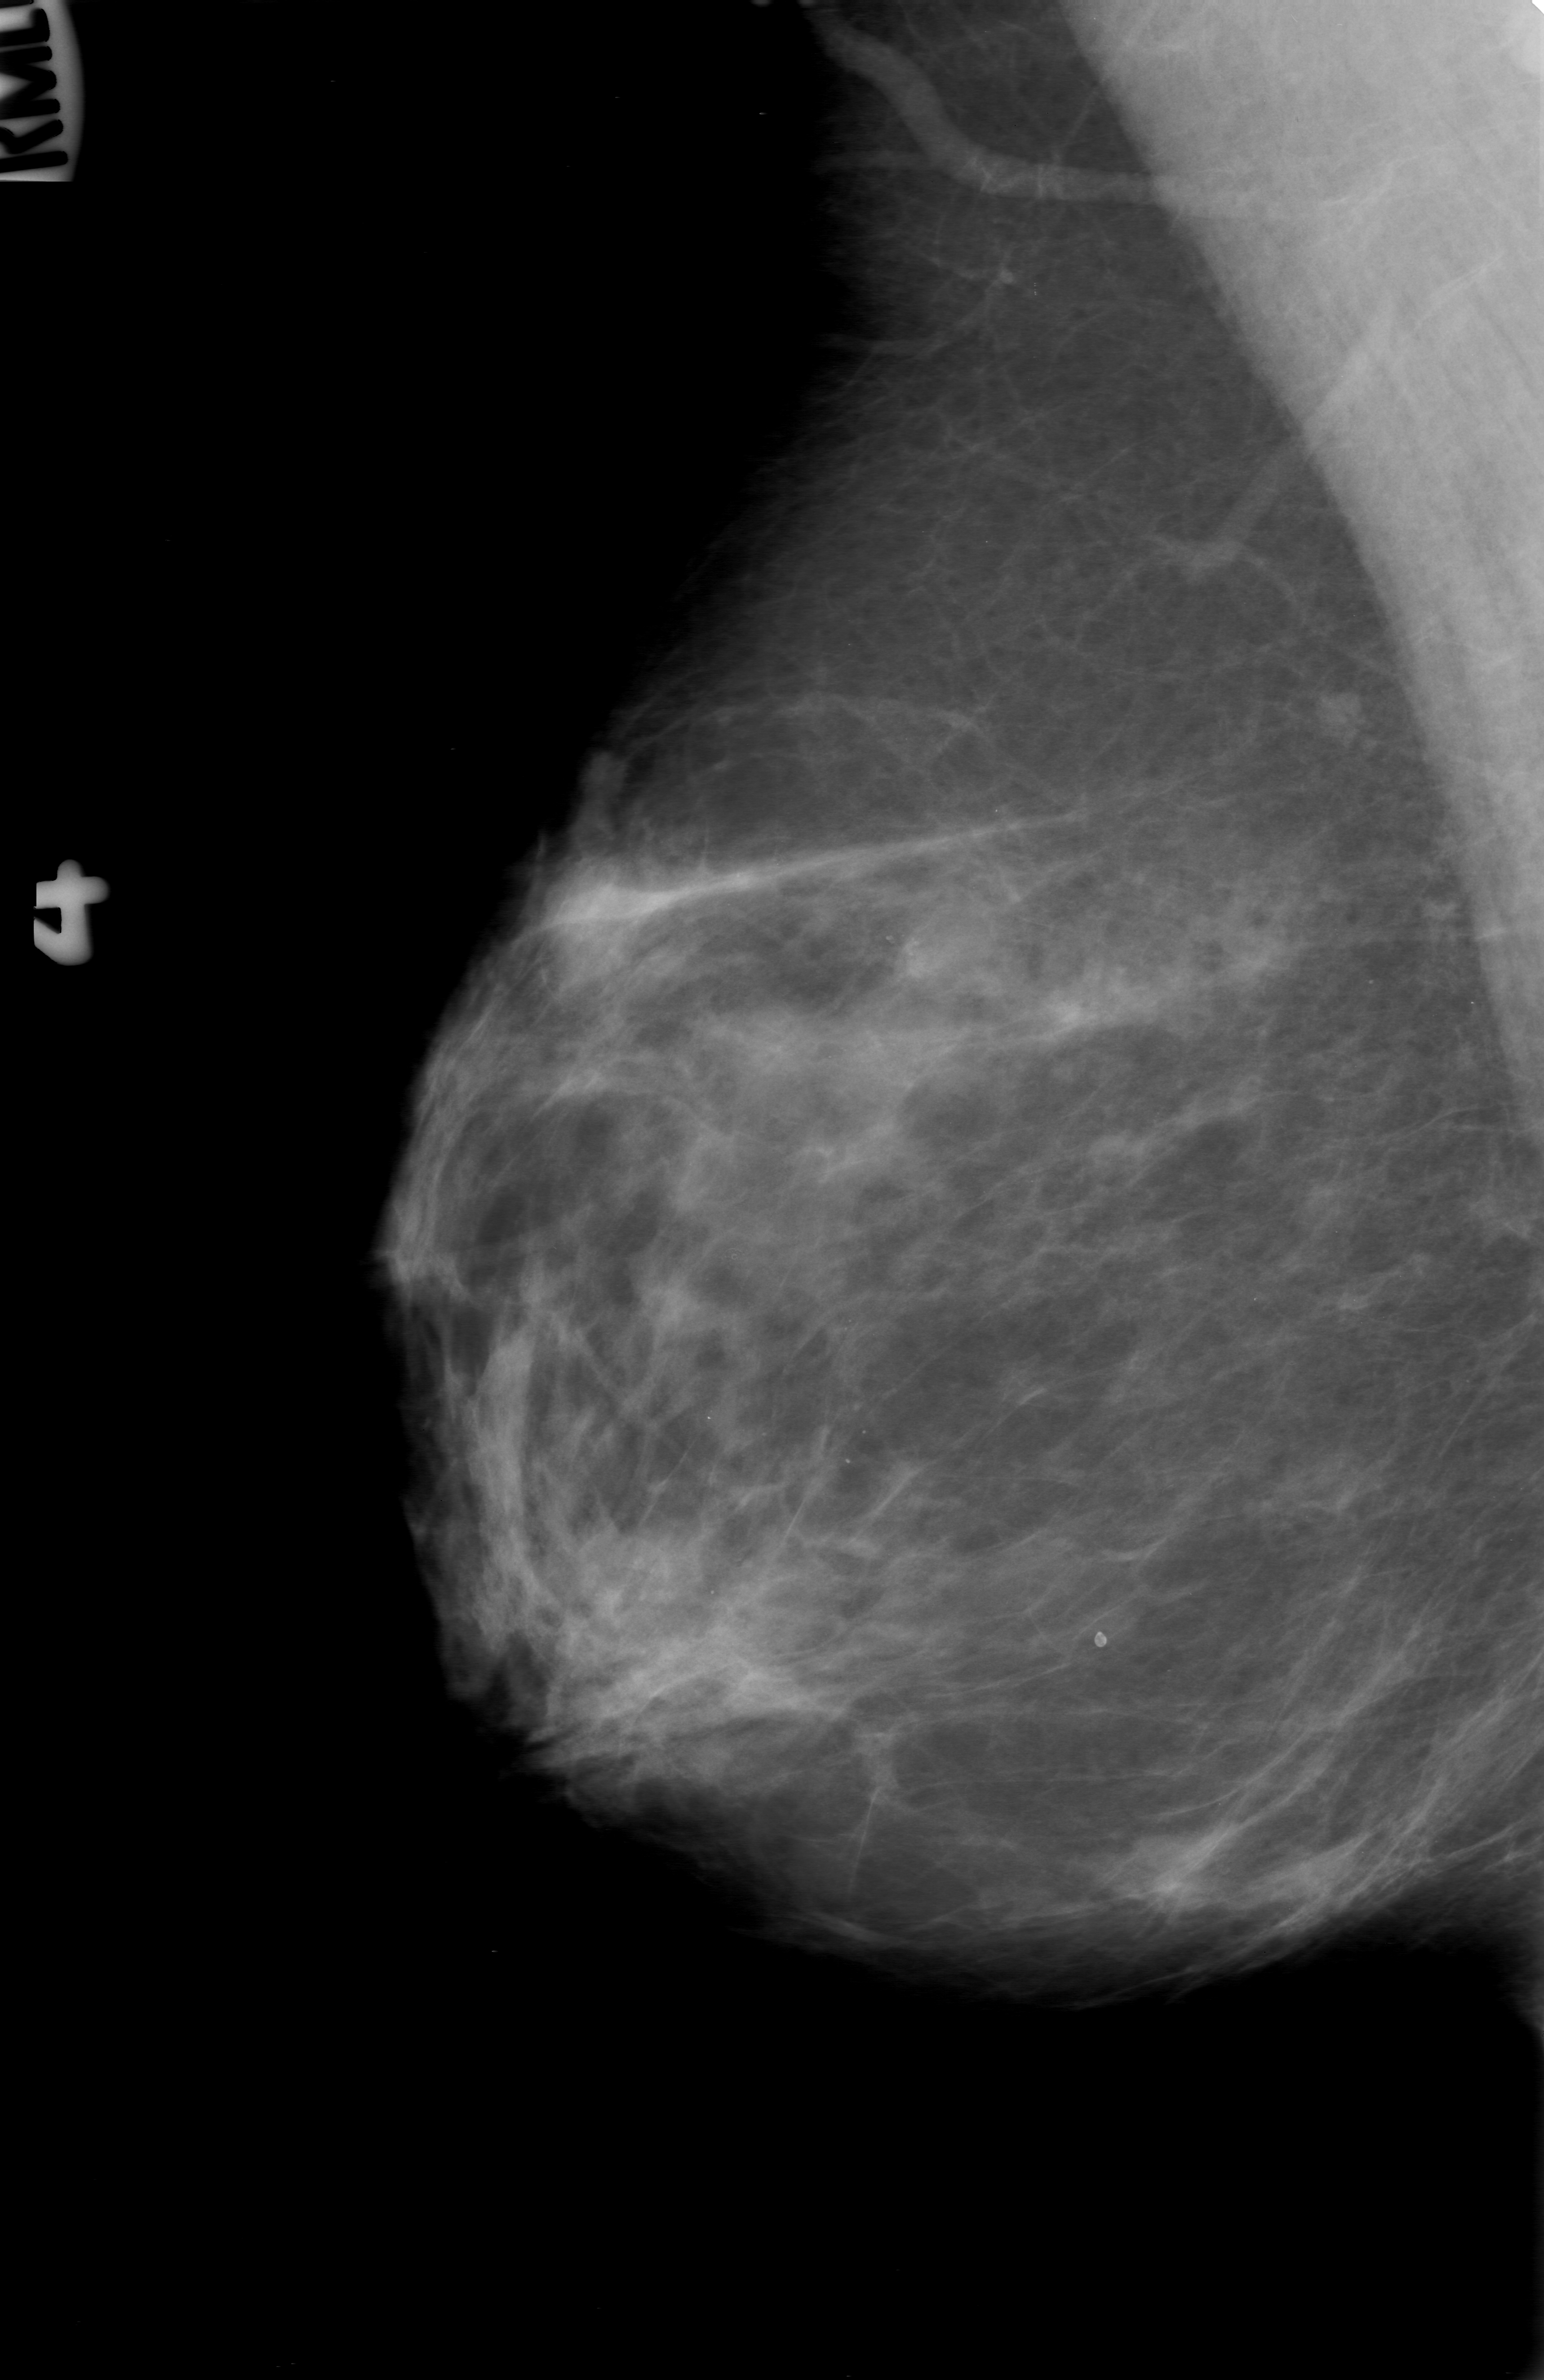
Mammogram (digitized film), right breast, mediolateral oblique (MLO) view, BI-RADS breast density category 2 (scale 1–4).
- Radiologist-marked abnormalities on this image: mass, shape lobulated, margins obscured; BI-RADS assessment category 0; pathology (as recorded): benign.